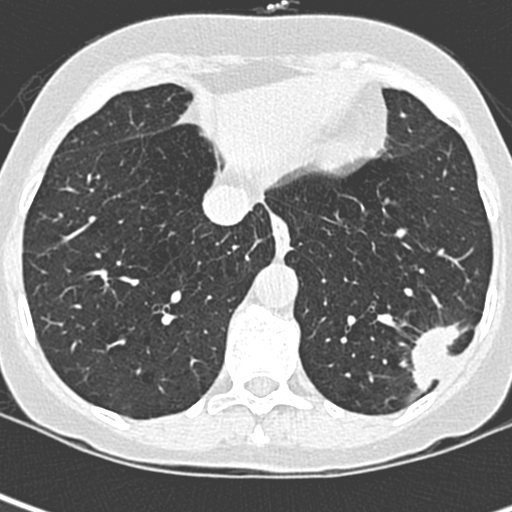
Low-dose screening chest CT, one axial slice. Position 81 of 252 along the scan axis. 120 kVp. Lung window (W 1500 / L -600 HU). 512 × 512 image matrix, field of view 271 × 271 mm.
Structures marked on this image (expert manual segmentation):
- lesion 1 (tumor, lower lobe of left lung): bounding box [x1, y1, x2, y2] px = [411, 323, 465, 393]